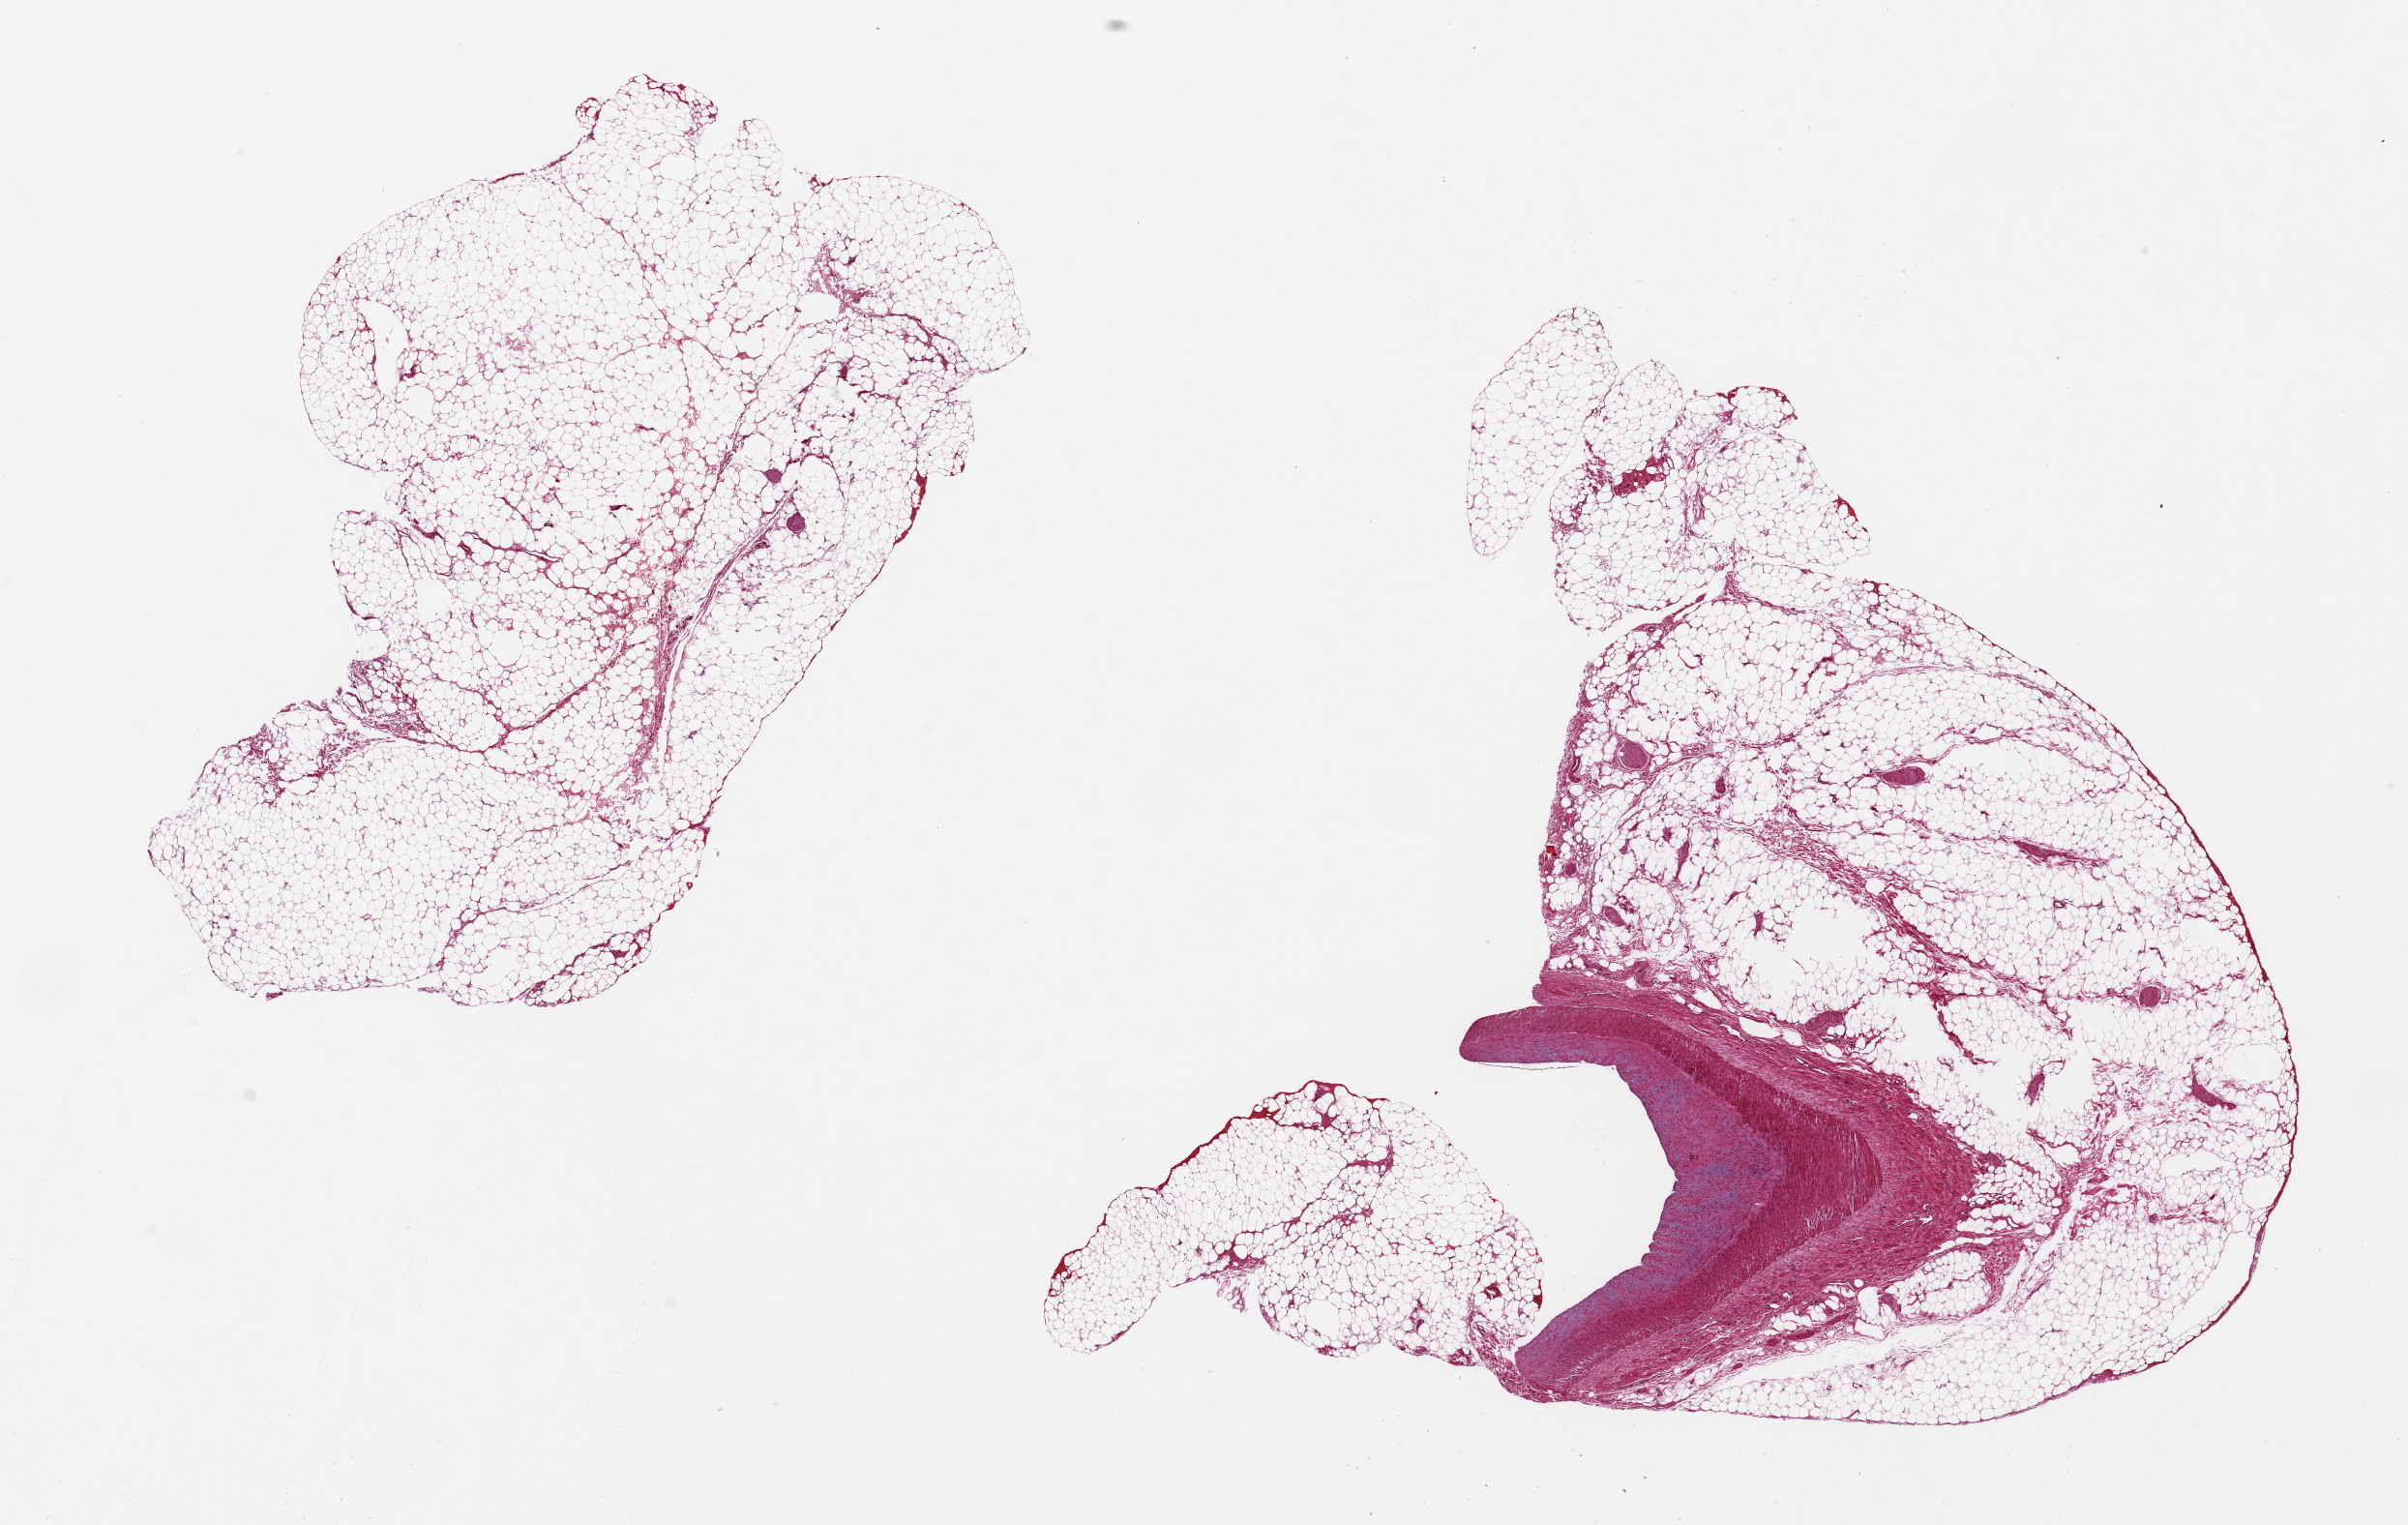
H&E whole-slide image — whole scanned area (about 19.7 x 12.5 mm, acquisition: 20x scan) shown as a low-resolution overview; PAXgene-fixed paraffin-embedded (PFPE) section; section of prostate (target tissue); tissue donor sample.
Review note (as recorded): 2 pieces, no prostate present, only fat/vascular tissue, unknown provenance.